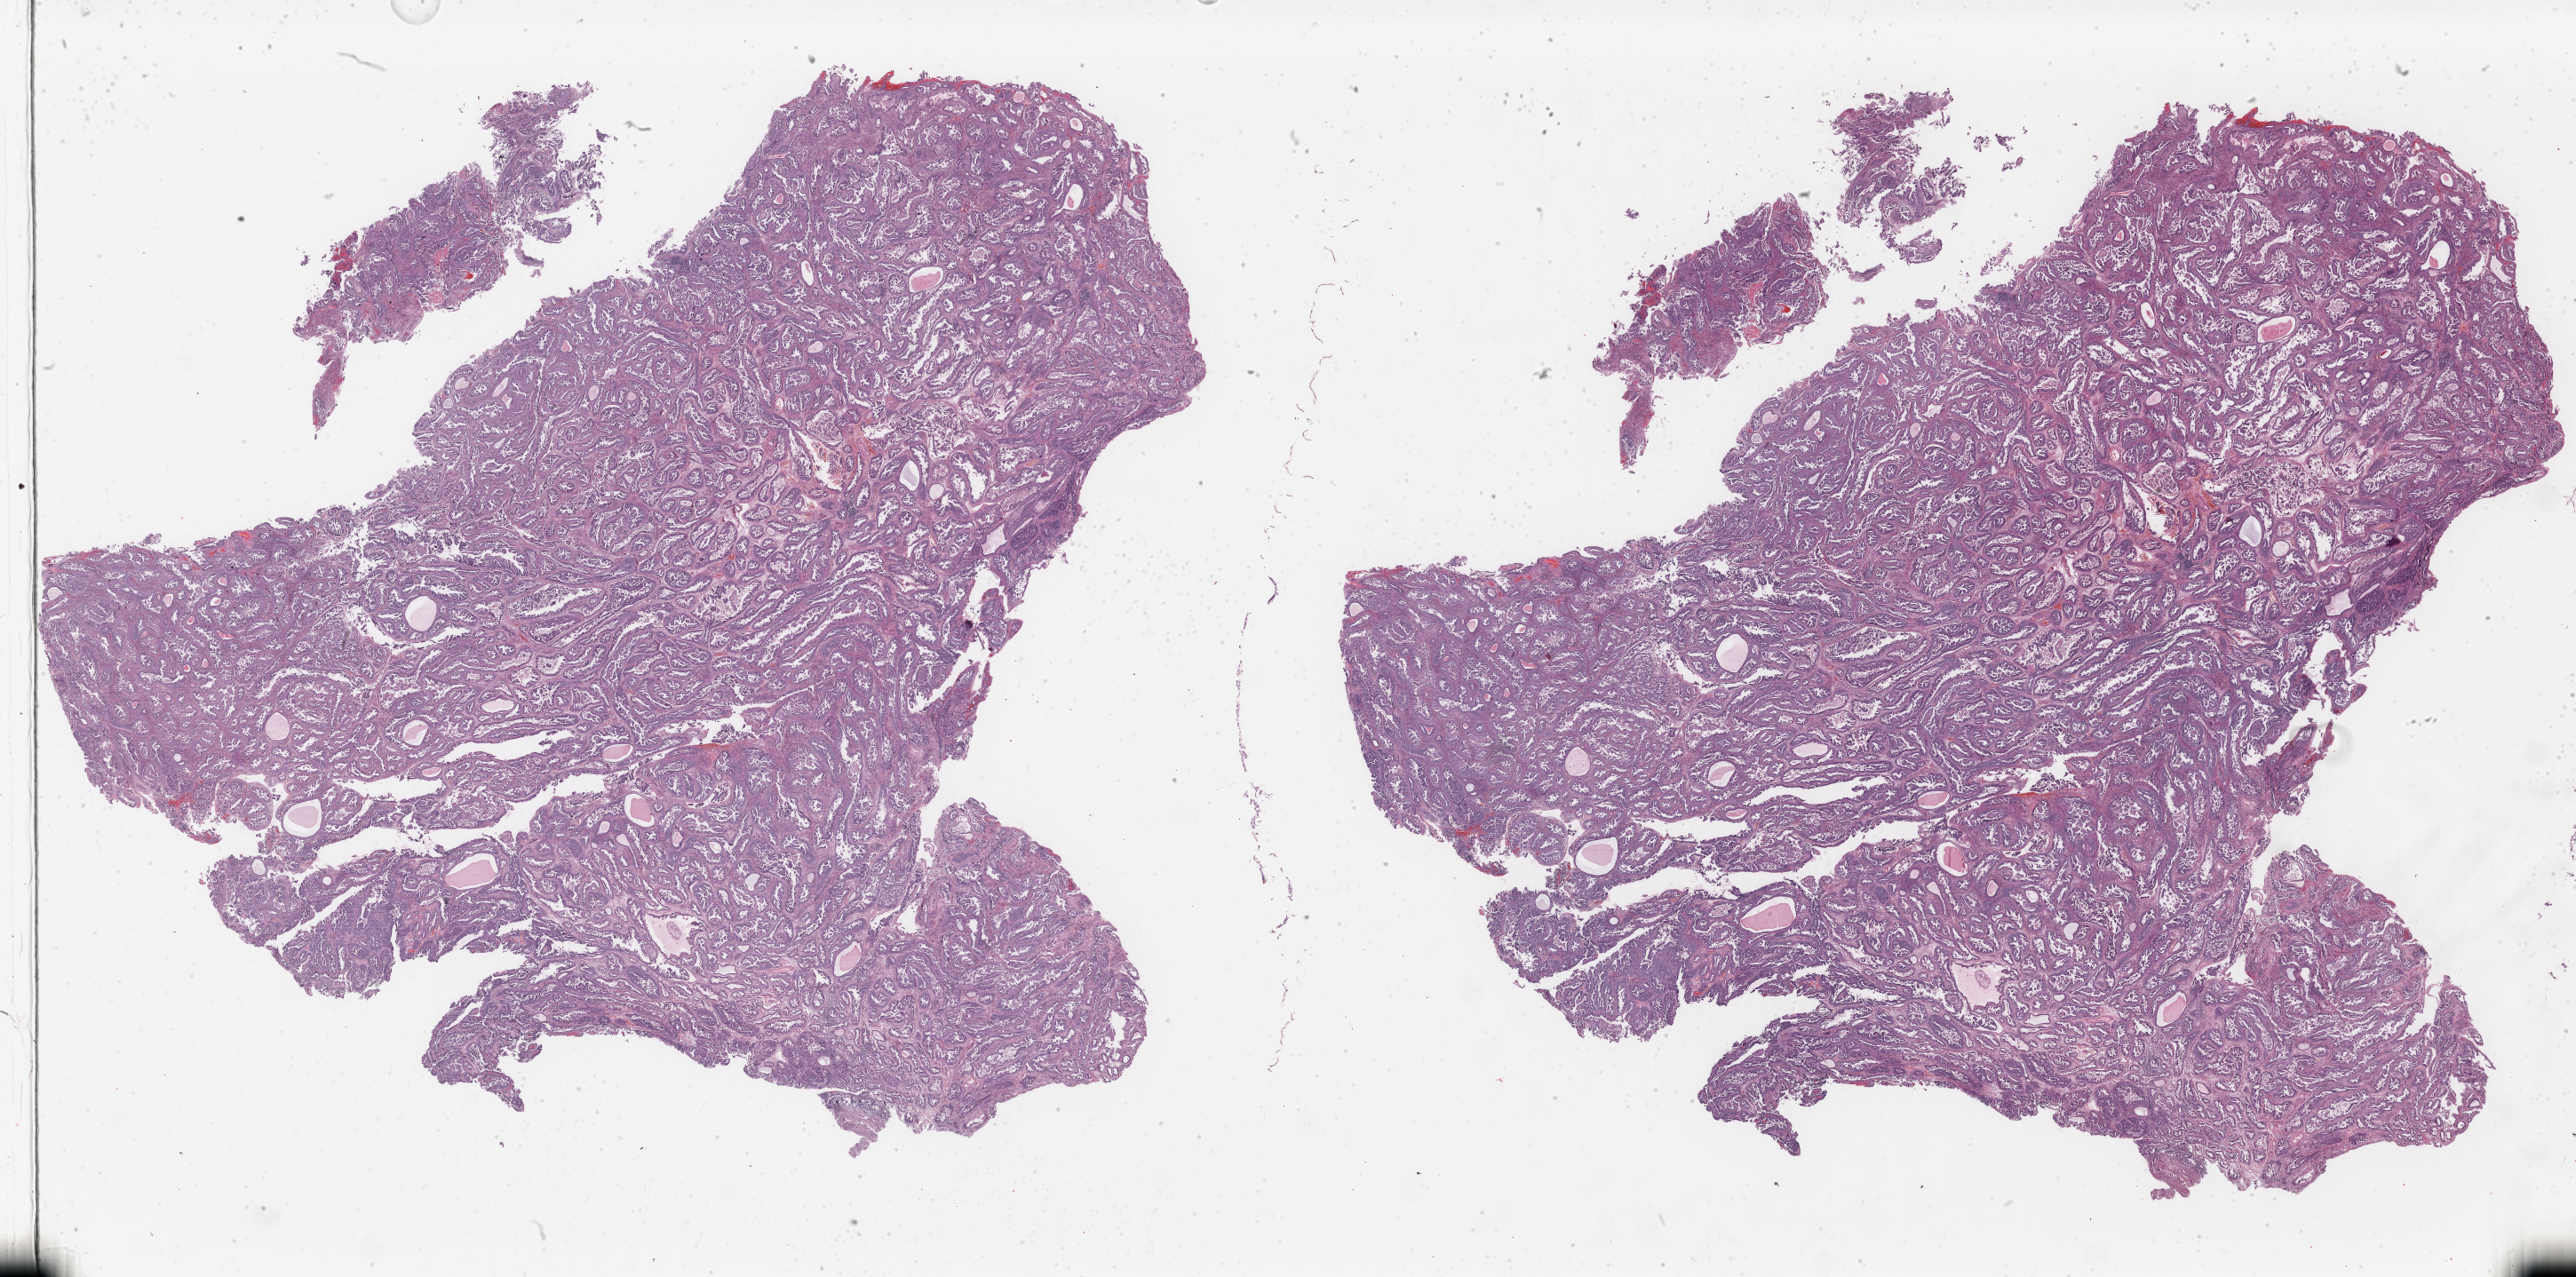
H&E whole-slide image — shown as a low-resolution overview of the whole scanned area (about 46.0 x 22.8 mm, acquisition: 40x scan). Formalin-fixed paraffin-embedded (FFPE) diagnostic section. Uterus, primary tumour sample. Patient: female, age at initial diagnosis 64 years. Histologic grade: G3 (poorly differentiated).
* FIGO stage: IIIC1
* lymph nodes positive (case pathology): 0 of 3 examined
* diagnosis: Serous cystadenocarcinoma, NOS